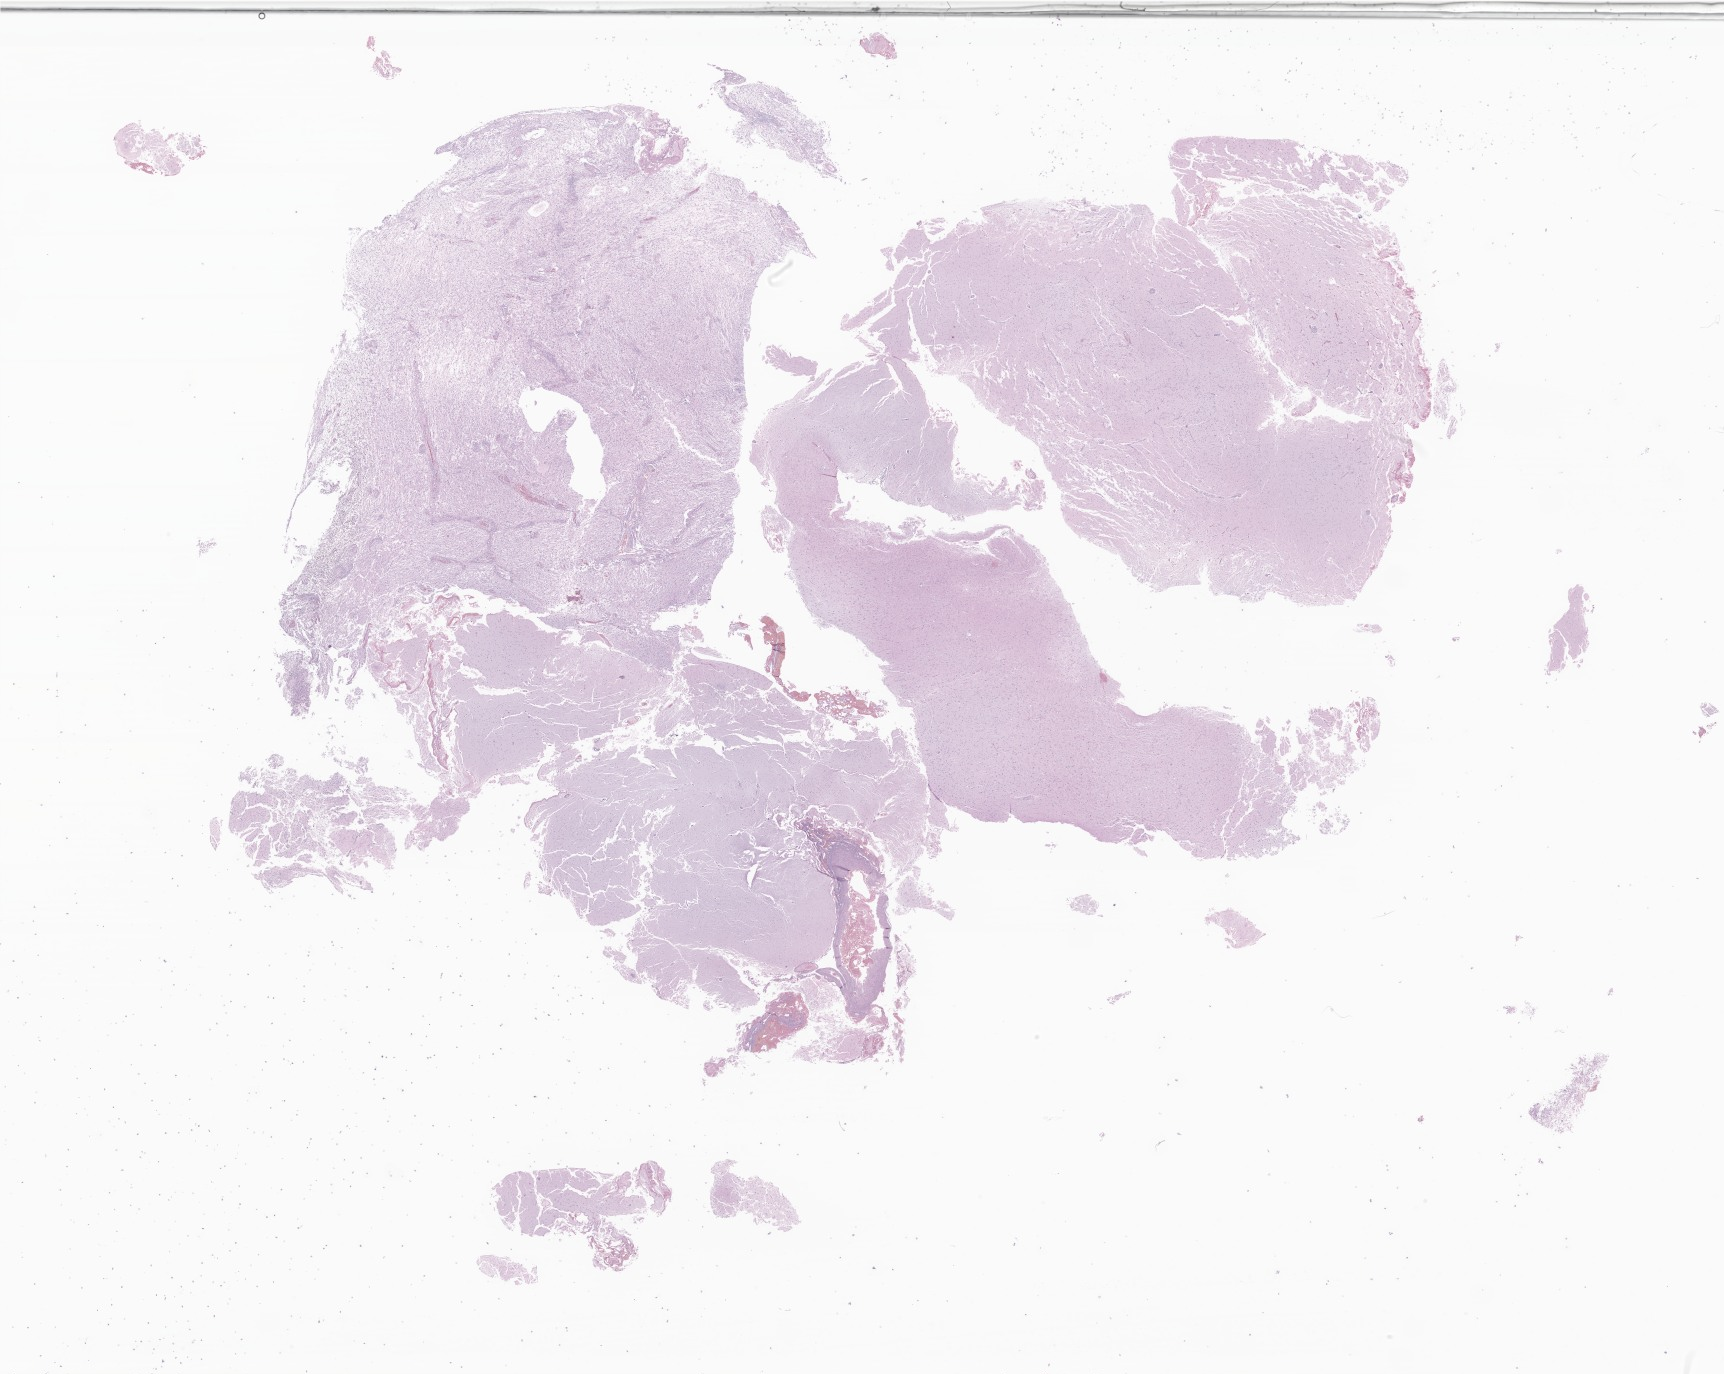
H&E whole-slide image of tumor tissue from the temporal lobe, low-resolution overview of the scanned area, about 29.1 x 23.2 mm, formalin-fixed, paraffin-embedded (FFPE) tissue. Male patient, age 174 months.
Diagnosis: Ganglioglioma, NOS.